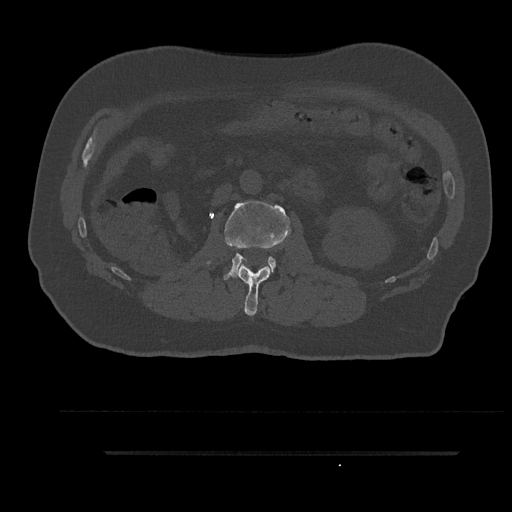
CT including the spine, one axial slice. Slice 138 of 797 in the series (ordered by position). Reconstruction kernel Br40s/3. 120 kVp. Bone window (W 1800 / L 400 HU). 512 × 512 image matrix. Male patient, age 63 years. From the clinical record (not read from this slice): primary cancer: renal; vertebrae with lytic lesions (as recorded): T8.
Structures marked on this image (semi-automatic segmentation, software-assisted and operator-edited):
- L1 vertebra: box from (x=236, y=264) to (x=272, y=316) px
- L2 vertebra: (x=224, y=201)–(x=291, y=280)